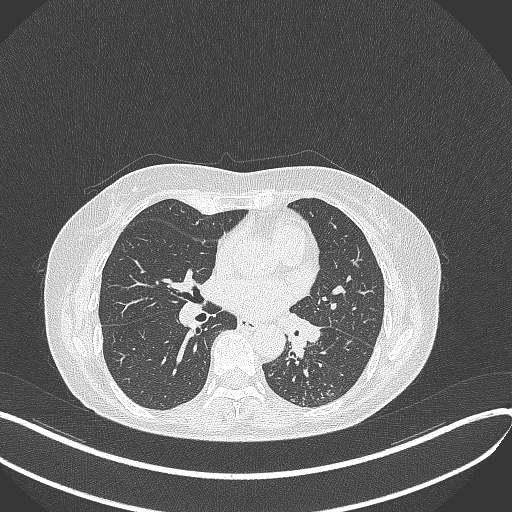
Chest CT, one axial slice. Position 206 of 429 along the scan axis. Reconstruction kernel B70f. Lung window (W 1500 / L -600 HU). 512 × 512 image matrix. Patient: female, 63 years. Case-level facts recorded for this patient, not image findings: clinical TNM (as recorded): T1b N0 M0.
Structures marked on this image (bounding box drawn by a radiologist):
- lung tumour (recorded histology: adenocarcinoma): bounding box (x1, y1, x2, y2) in pixels: (279, 316, 319, 361)